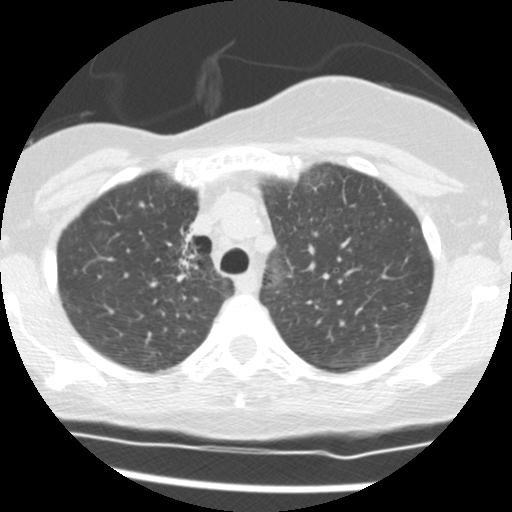
Low-dose screening chest CT, axial slice. Second screening round (one year after baseline). Lung window (W 1500 / L -600 HU). 2.5 mm slice thickness. Standard (soft-tissue) reconstruction kernel (STANDARD). 120 kVp. Slice 30 of 165 in the series. Female, age 56 years at enrolment. Current smoker at enrolment.
- Expert-annotated lung lesion, bounding box (x1, y1, x2, y2) in pixels: (156, 218, 217, 287).
- The screening reader recorded 2 non-calcified nodules or masses ≥4 mm on this exam (right middle lobe, right lower lobe); which of them this box marks is not recorded.
- Official screen result: positive, change unspecified: nodule(s) >= 4 mm or enlarging nodule(s), mass(es), or other non-specific abnormalities suspicious for lung cancer.